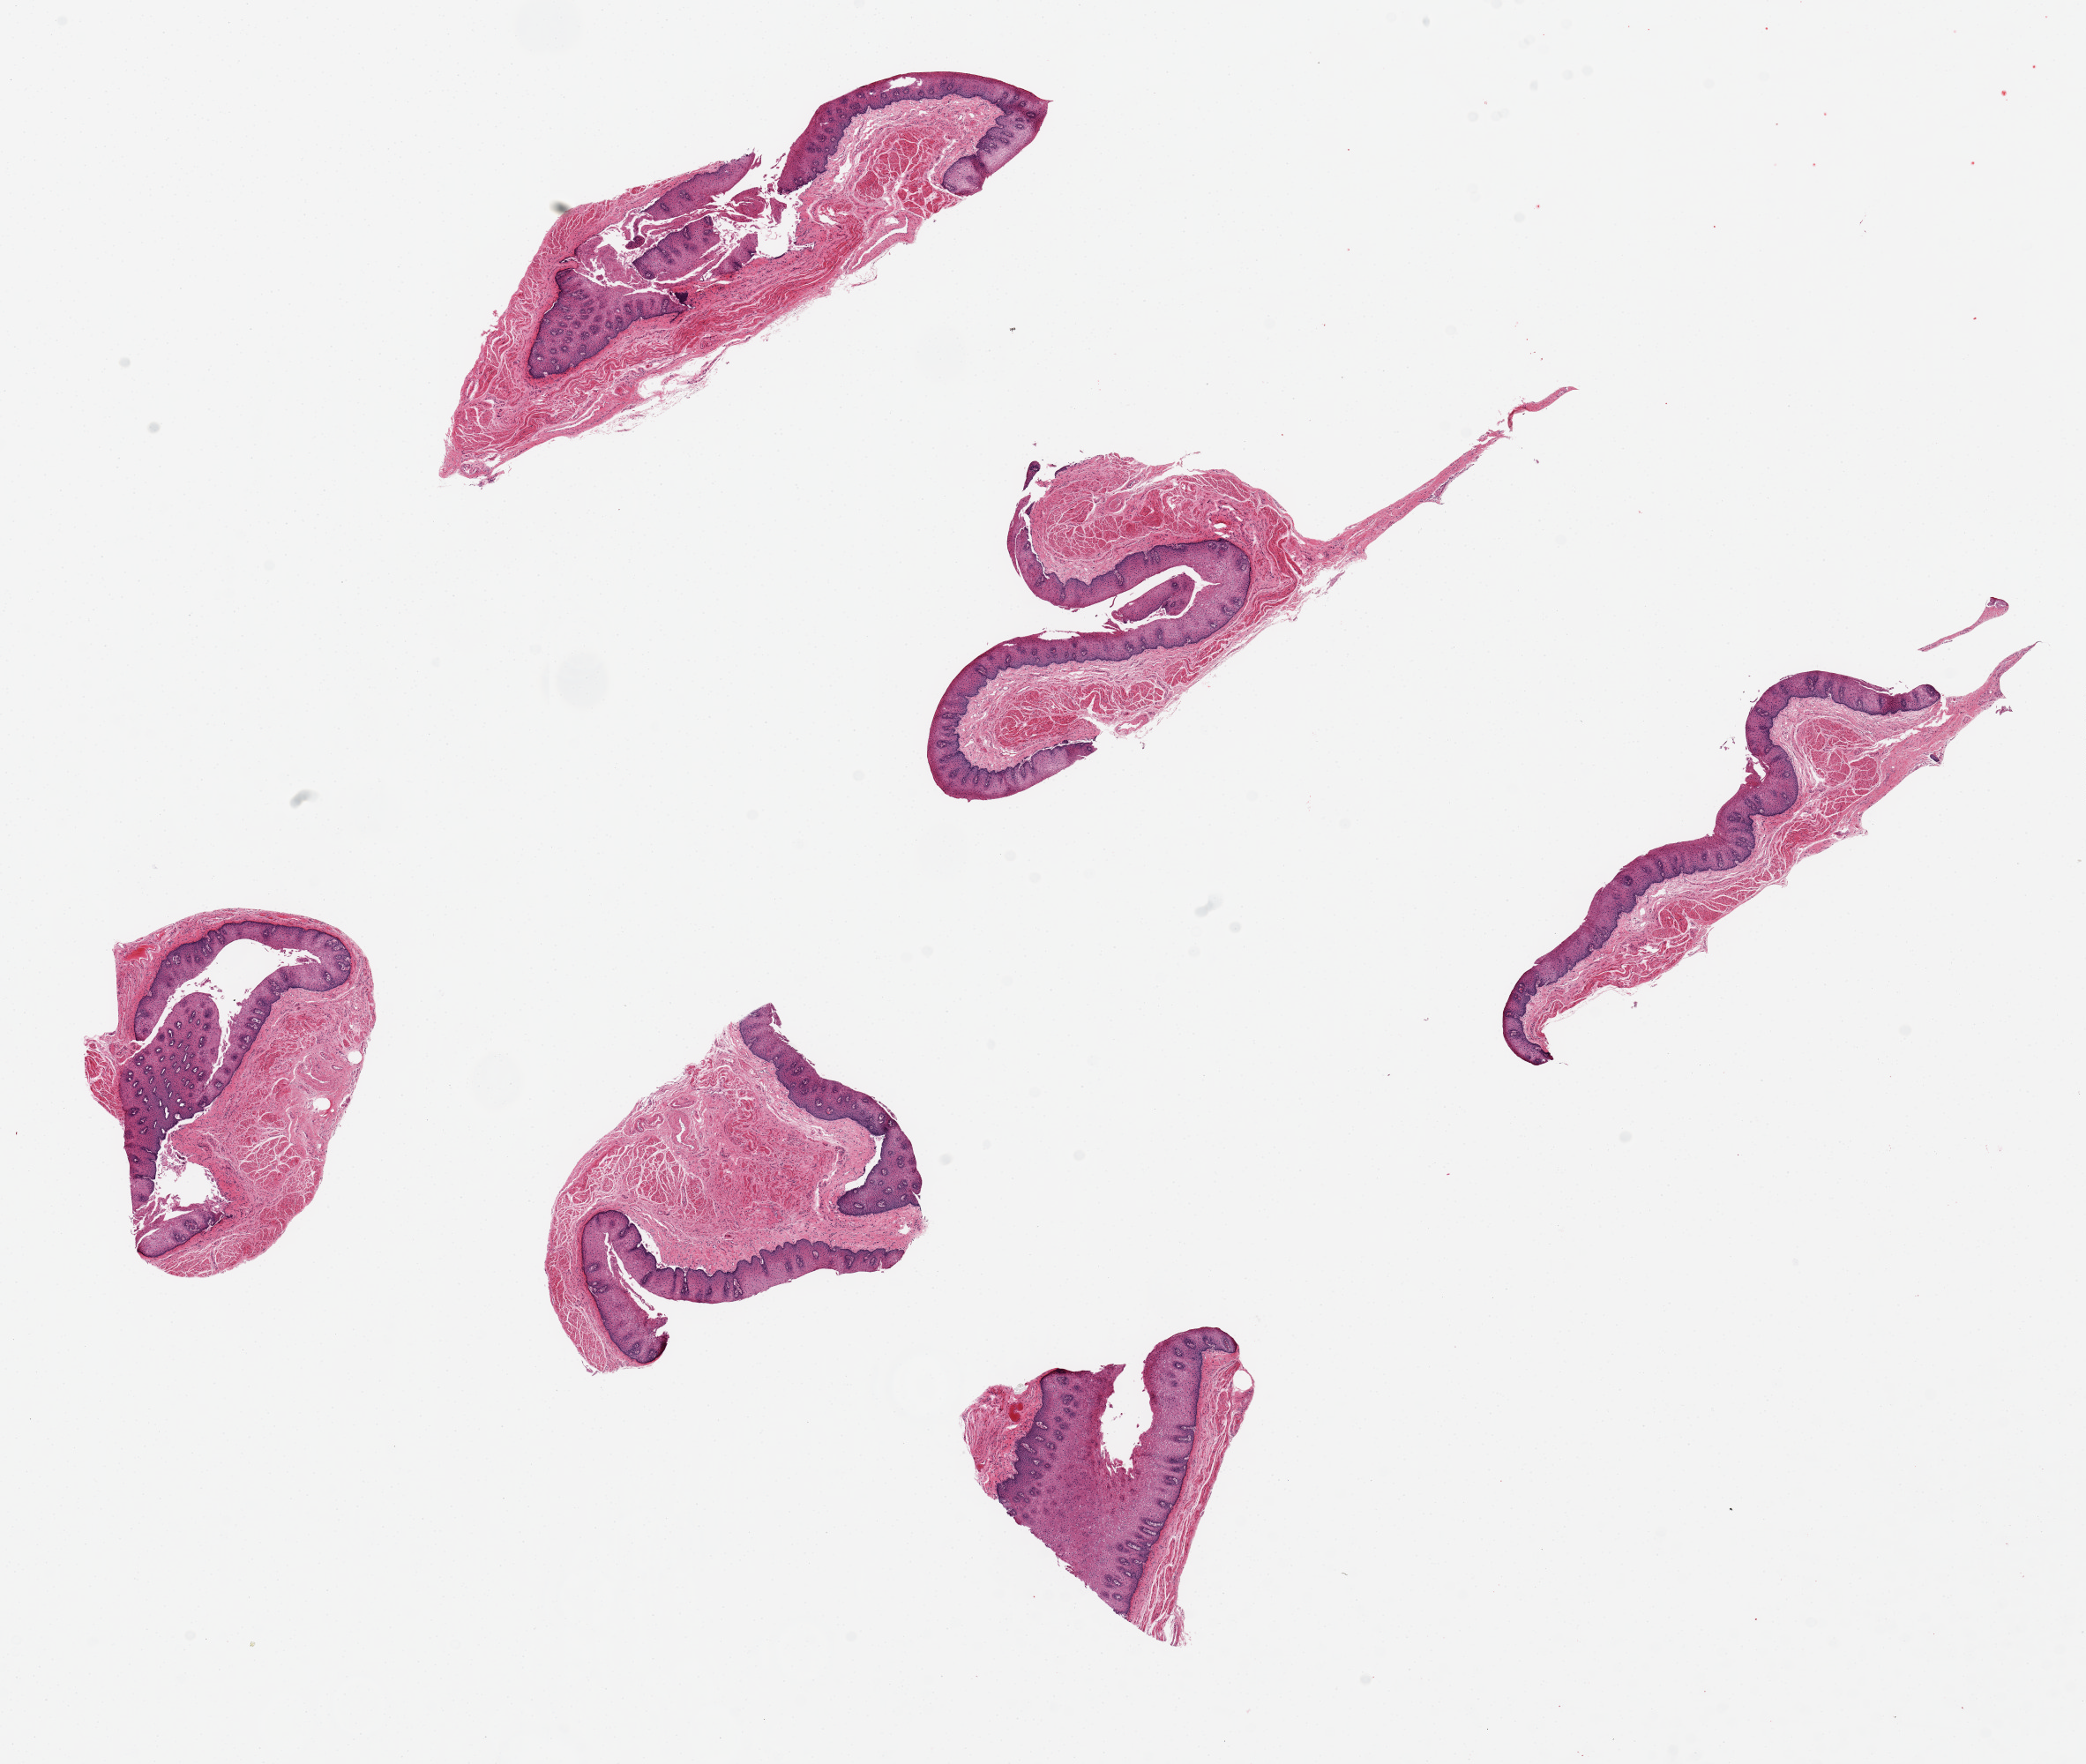
H&E whole-slide image — a low-resolution overview of the entire scanned area, about 18.7 x 15.8 mm; PAXgene-fixed, paraffin-embedded tissue; sampled site (target tissue): esophageal mucous membrane; tissue donor sample.
Reviewer comment on this tissue sample: 6 ~ 5x1.5mm pieces; squamous mucosa is 10-20% of thickness.